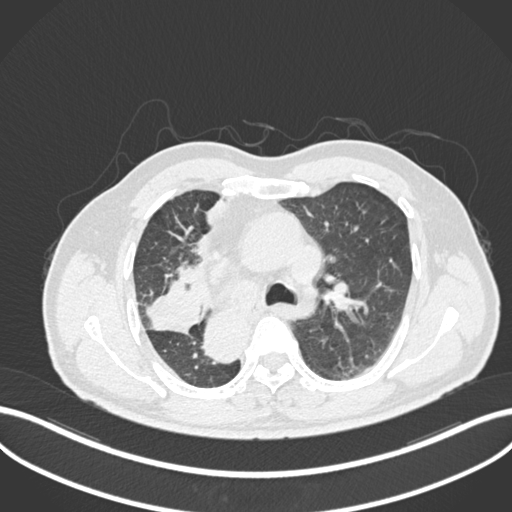
Chest CT, one axial slice; position 158 of 206 along the scan axis; lung window (W 1500 / L -600 HU); 1 mm slice thickness; 512 × 512 image matrix, field of view 400 × 400 mm. Male patient, age 67 years. From the clinical record (not read from this slice): clinical TNM (as recorded): T2a N0 M0.
Structures marked on this image (rectangle marked by the reading radiologist):
- lung tumour (recorded histology: squamous cell carcinoma): bounding box (x1, y1, x2, y2) in pixels: (144, 278, 203, 336)